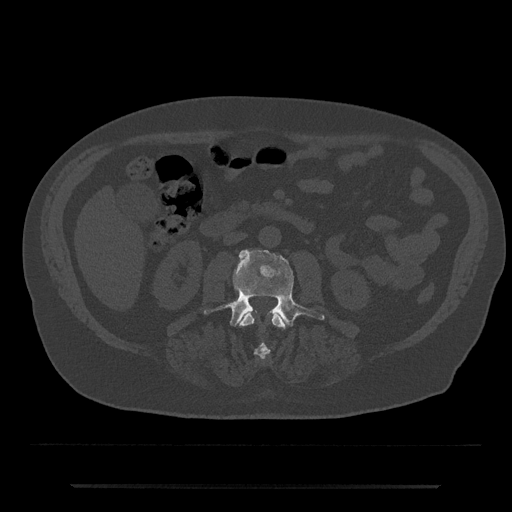
CT including the spine, one axial slice. Slice 428 of 797 in the series (ordered by position). 120 kVp. Bone window (W 1800 / L 400 HU). 512 × 512 image matrix. Male patient, age 80 years. Case-level facts recorded for this patient, not image findings: primary cancer: prostate.
Annotated regions visible in this slice (semi-automatically segmented with operator editing):
- L2 vertebra: bounding box <240,311,285,359> (left, top, right, bottom; pixels)
- L3 vertebra: <204,249,325,328>